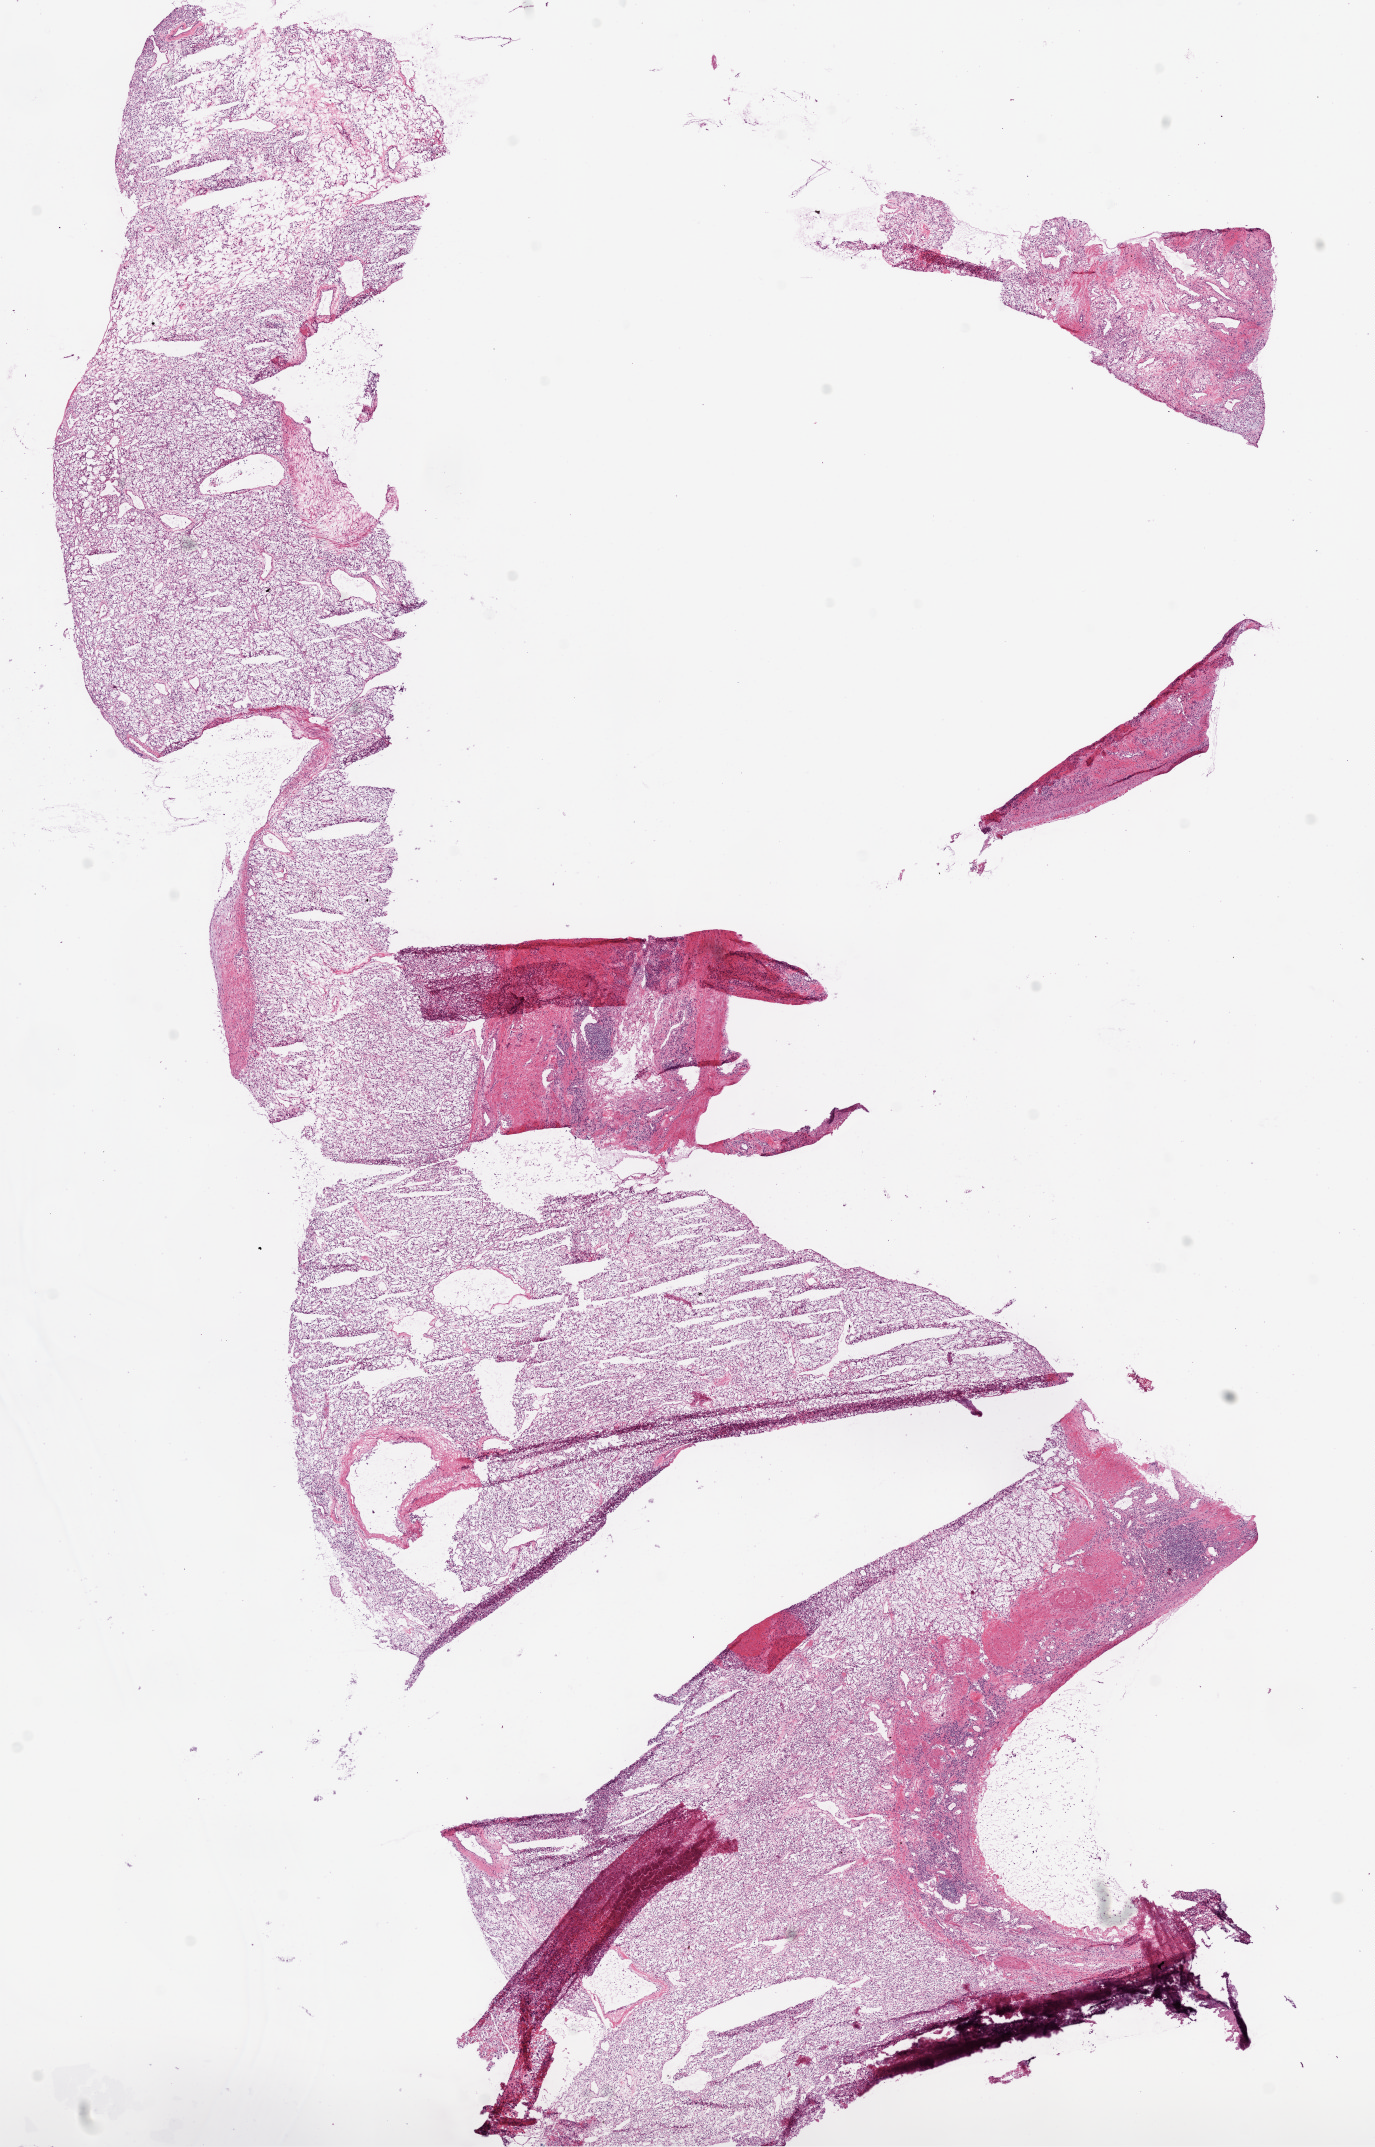
H&E whole-slide image, low-resolution overview of the scanned area, about 11.0 x 17.2 mm (slide scanned at 20x), frozen section, sample: primary tumour, kidney. Patient: female, age at initial diagnosis 76 years. Histologic grade: G2 (moderately differentiated). Slide review estimates, as recorded: tumour cells 85%, tumour nuclei 80%, normal cells 10%, stromal cells 5%, necrosis 0%.
Lymph nodes positive (case pathology): 0 of 2 examined. Histologic diagnosis: Clear cell adenocarcinoma, NOS. AJCC pathologic stage: II. TNM: T2 N0 M0.